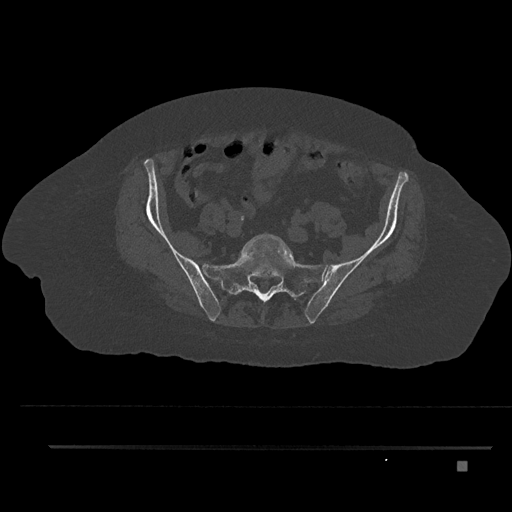
CT including the spine, one axial slice. Reconstruction kernel Br40s/3. Bone window (W 1800 / L 400 HU). 512 × 512 image matrix, field of view 437 × 437 mm. Patient: female, 76 years. From the clinical record (not read from this slice): primary cancer: lung; vertebrae with lytic lesions (as recorded): T11, L3.
Annotated regions visible in this slice (semi-automatic segmentation, software-assisted and operator-edited):
- L5 vertebra: bounding box [x1, y1, x2, y2] px = [243, 233, 293, 258]